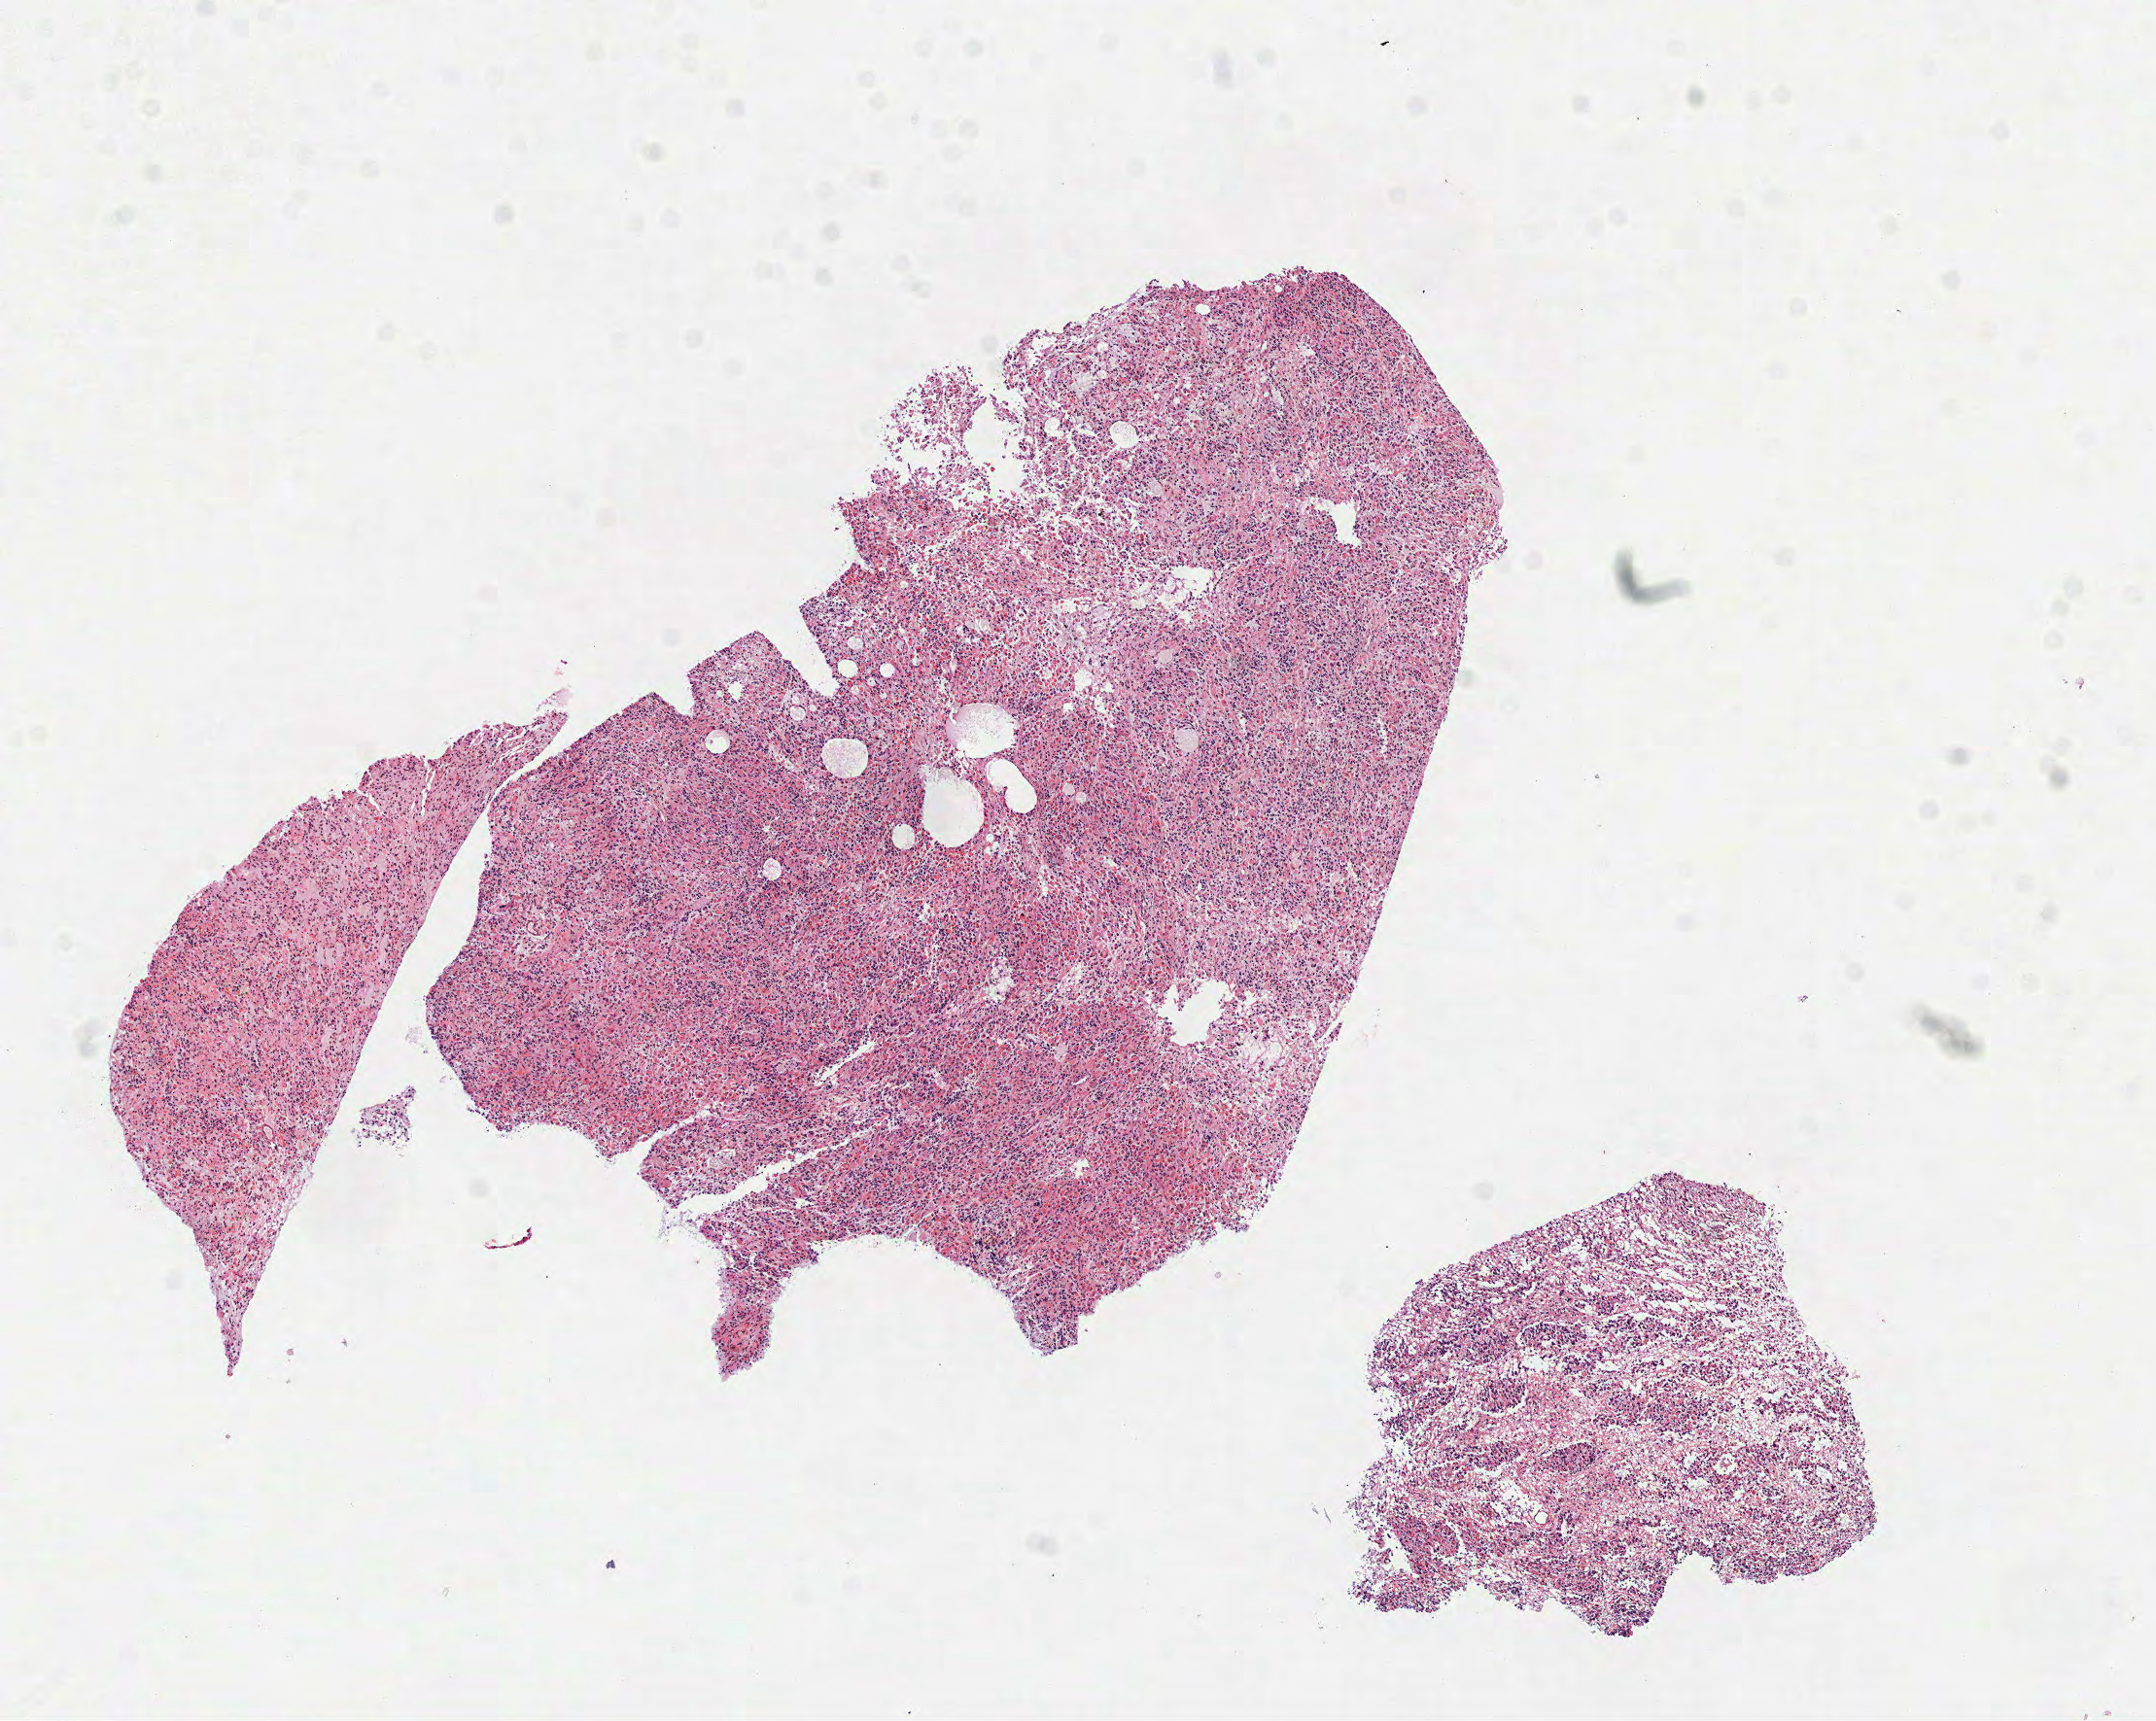
H&E-stained whole-slide image — low-resolution overview of the scanned area, about 8.9 x 7.1 mm. FFPE section. Primary tumour sample from the brain. Patient: female, age at initial diagnosis 49 years. Histologic grade: G3 (poorly differentiated).
- diagnosis: Mixed glioma